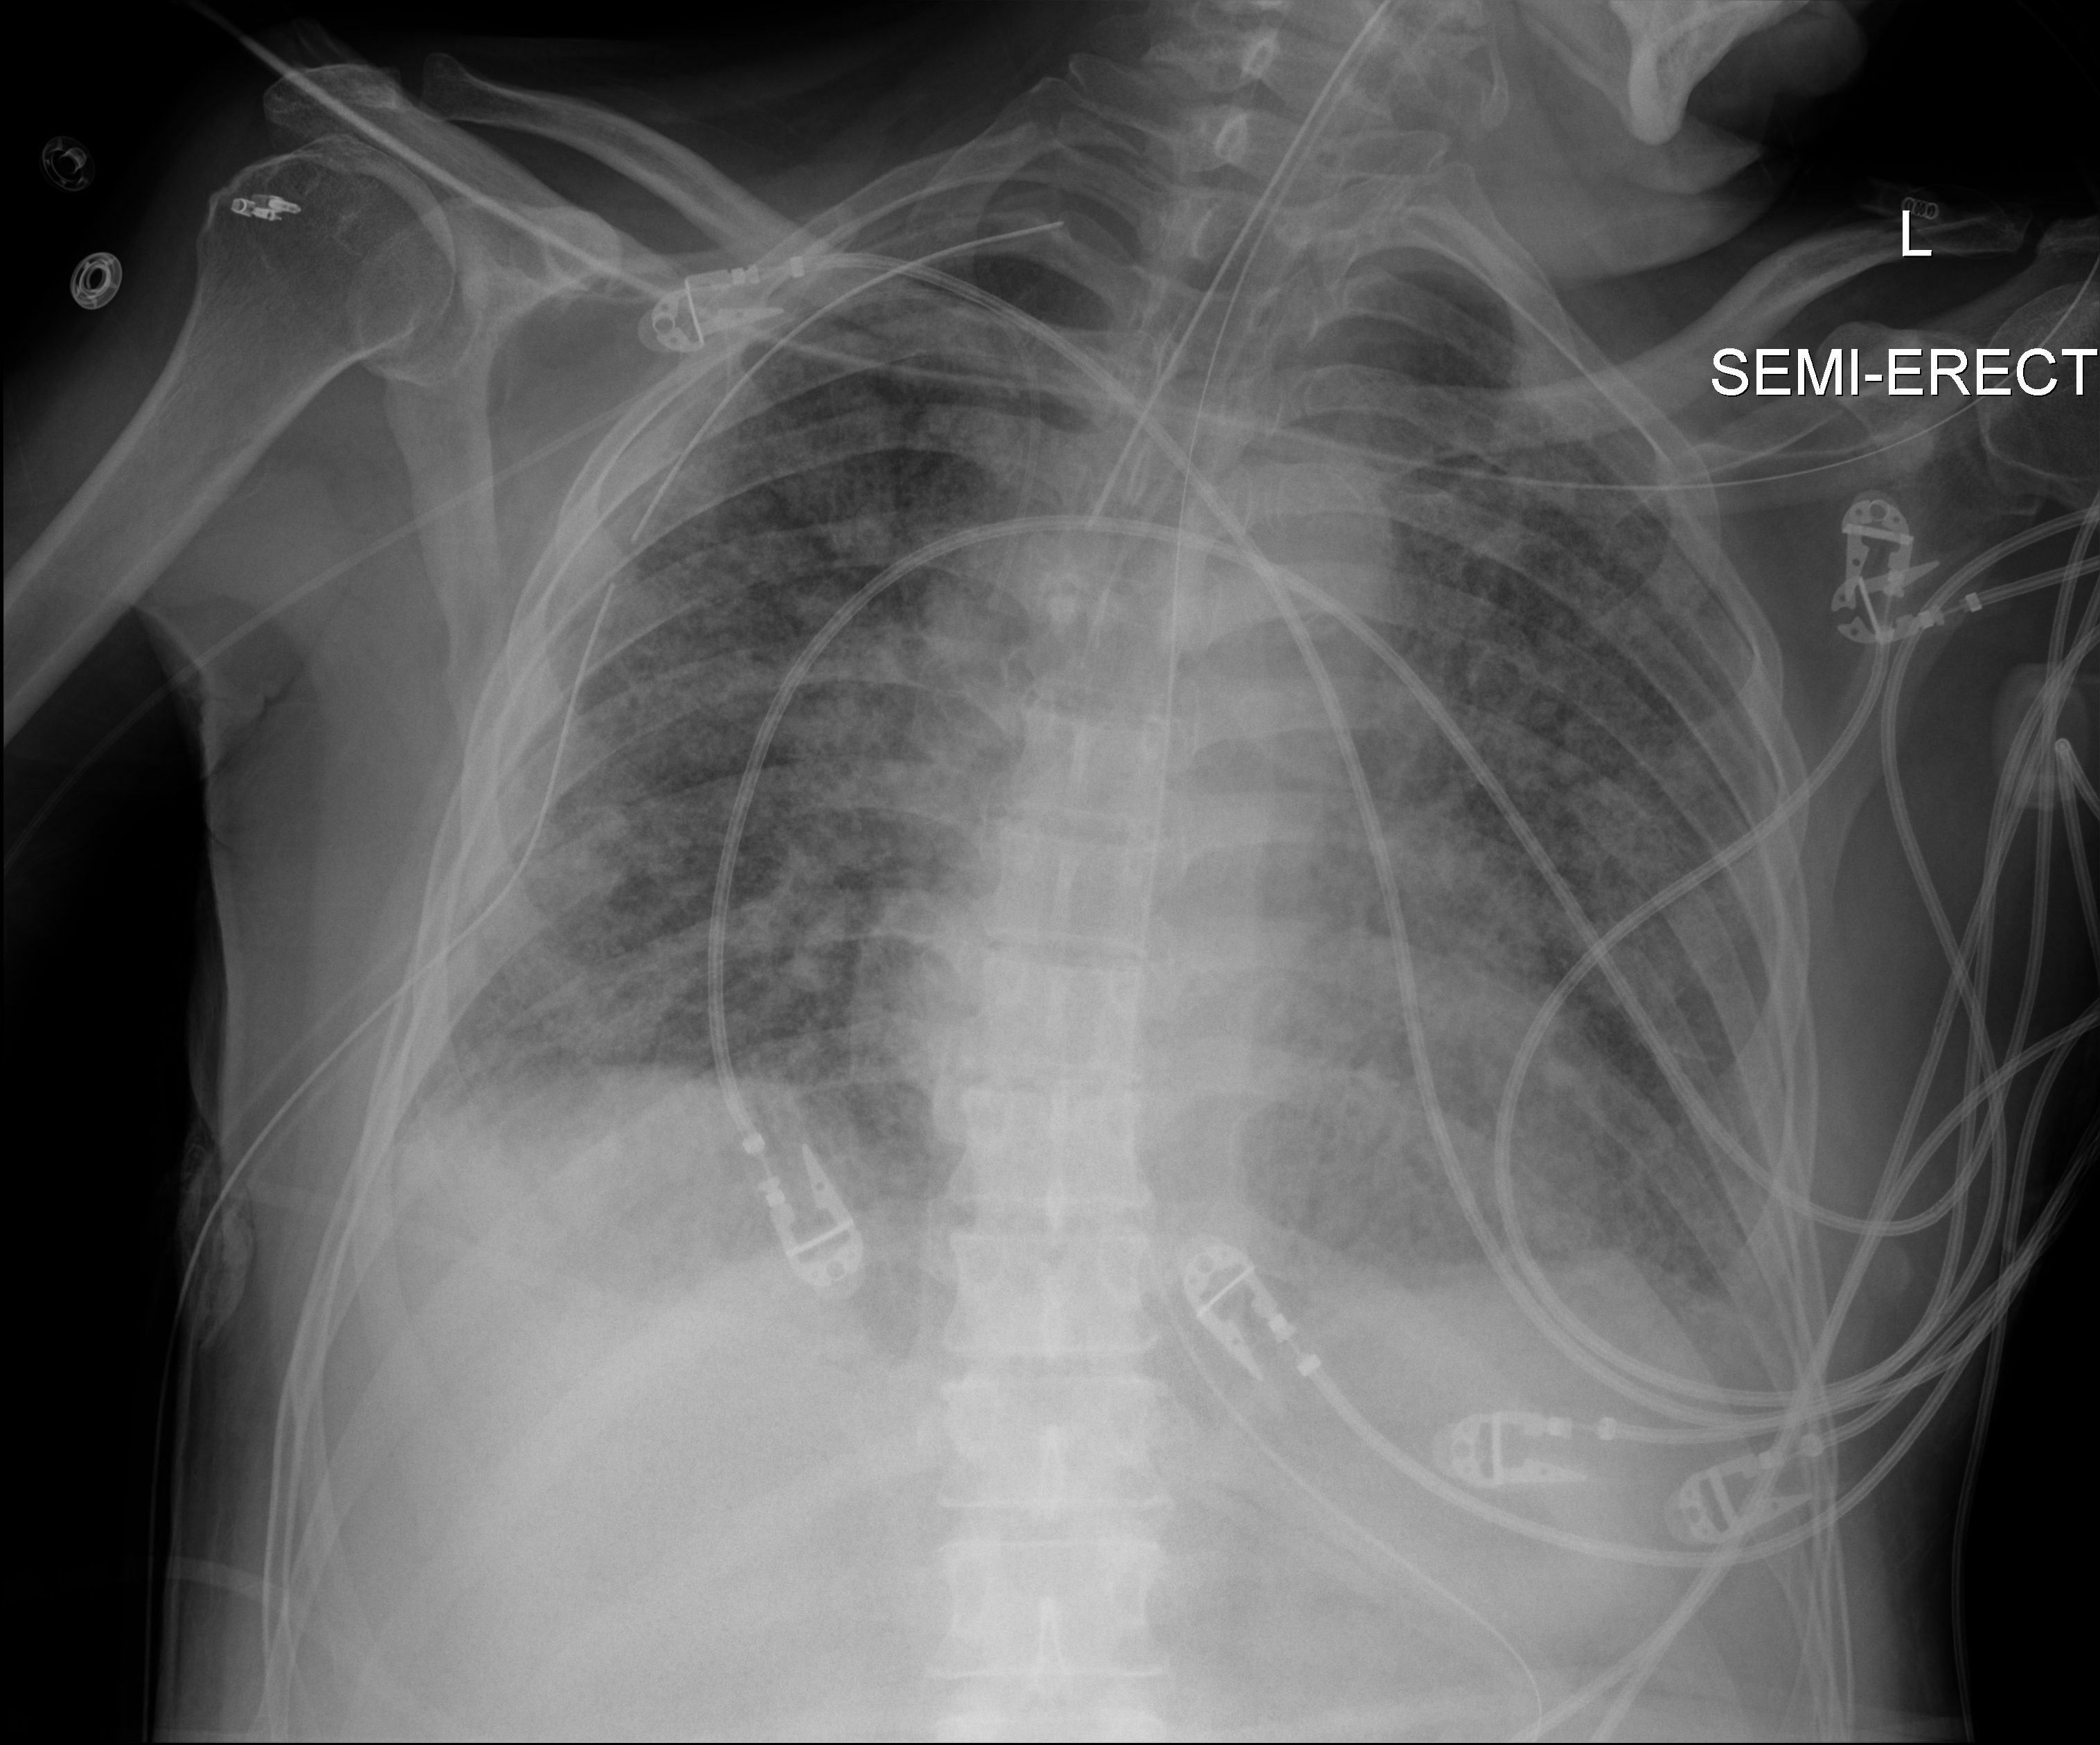
Chest X-ray (portable), anteroposterior (AP) projection. Male patient hospitalised with COVID-19, age 60–74 years.
Hospital-stay facts (about this admission, not read from this image; timing relative to this image not recorded):
- chronic kidney disease (admission record): no
- mechanically ventilated during this hospital stay: yes
- admitted to intensive care during this hospital stay: yes